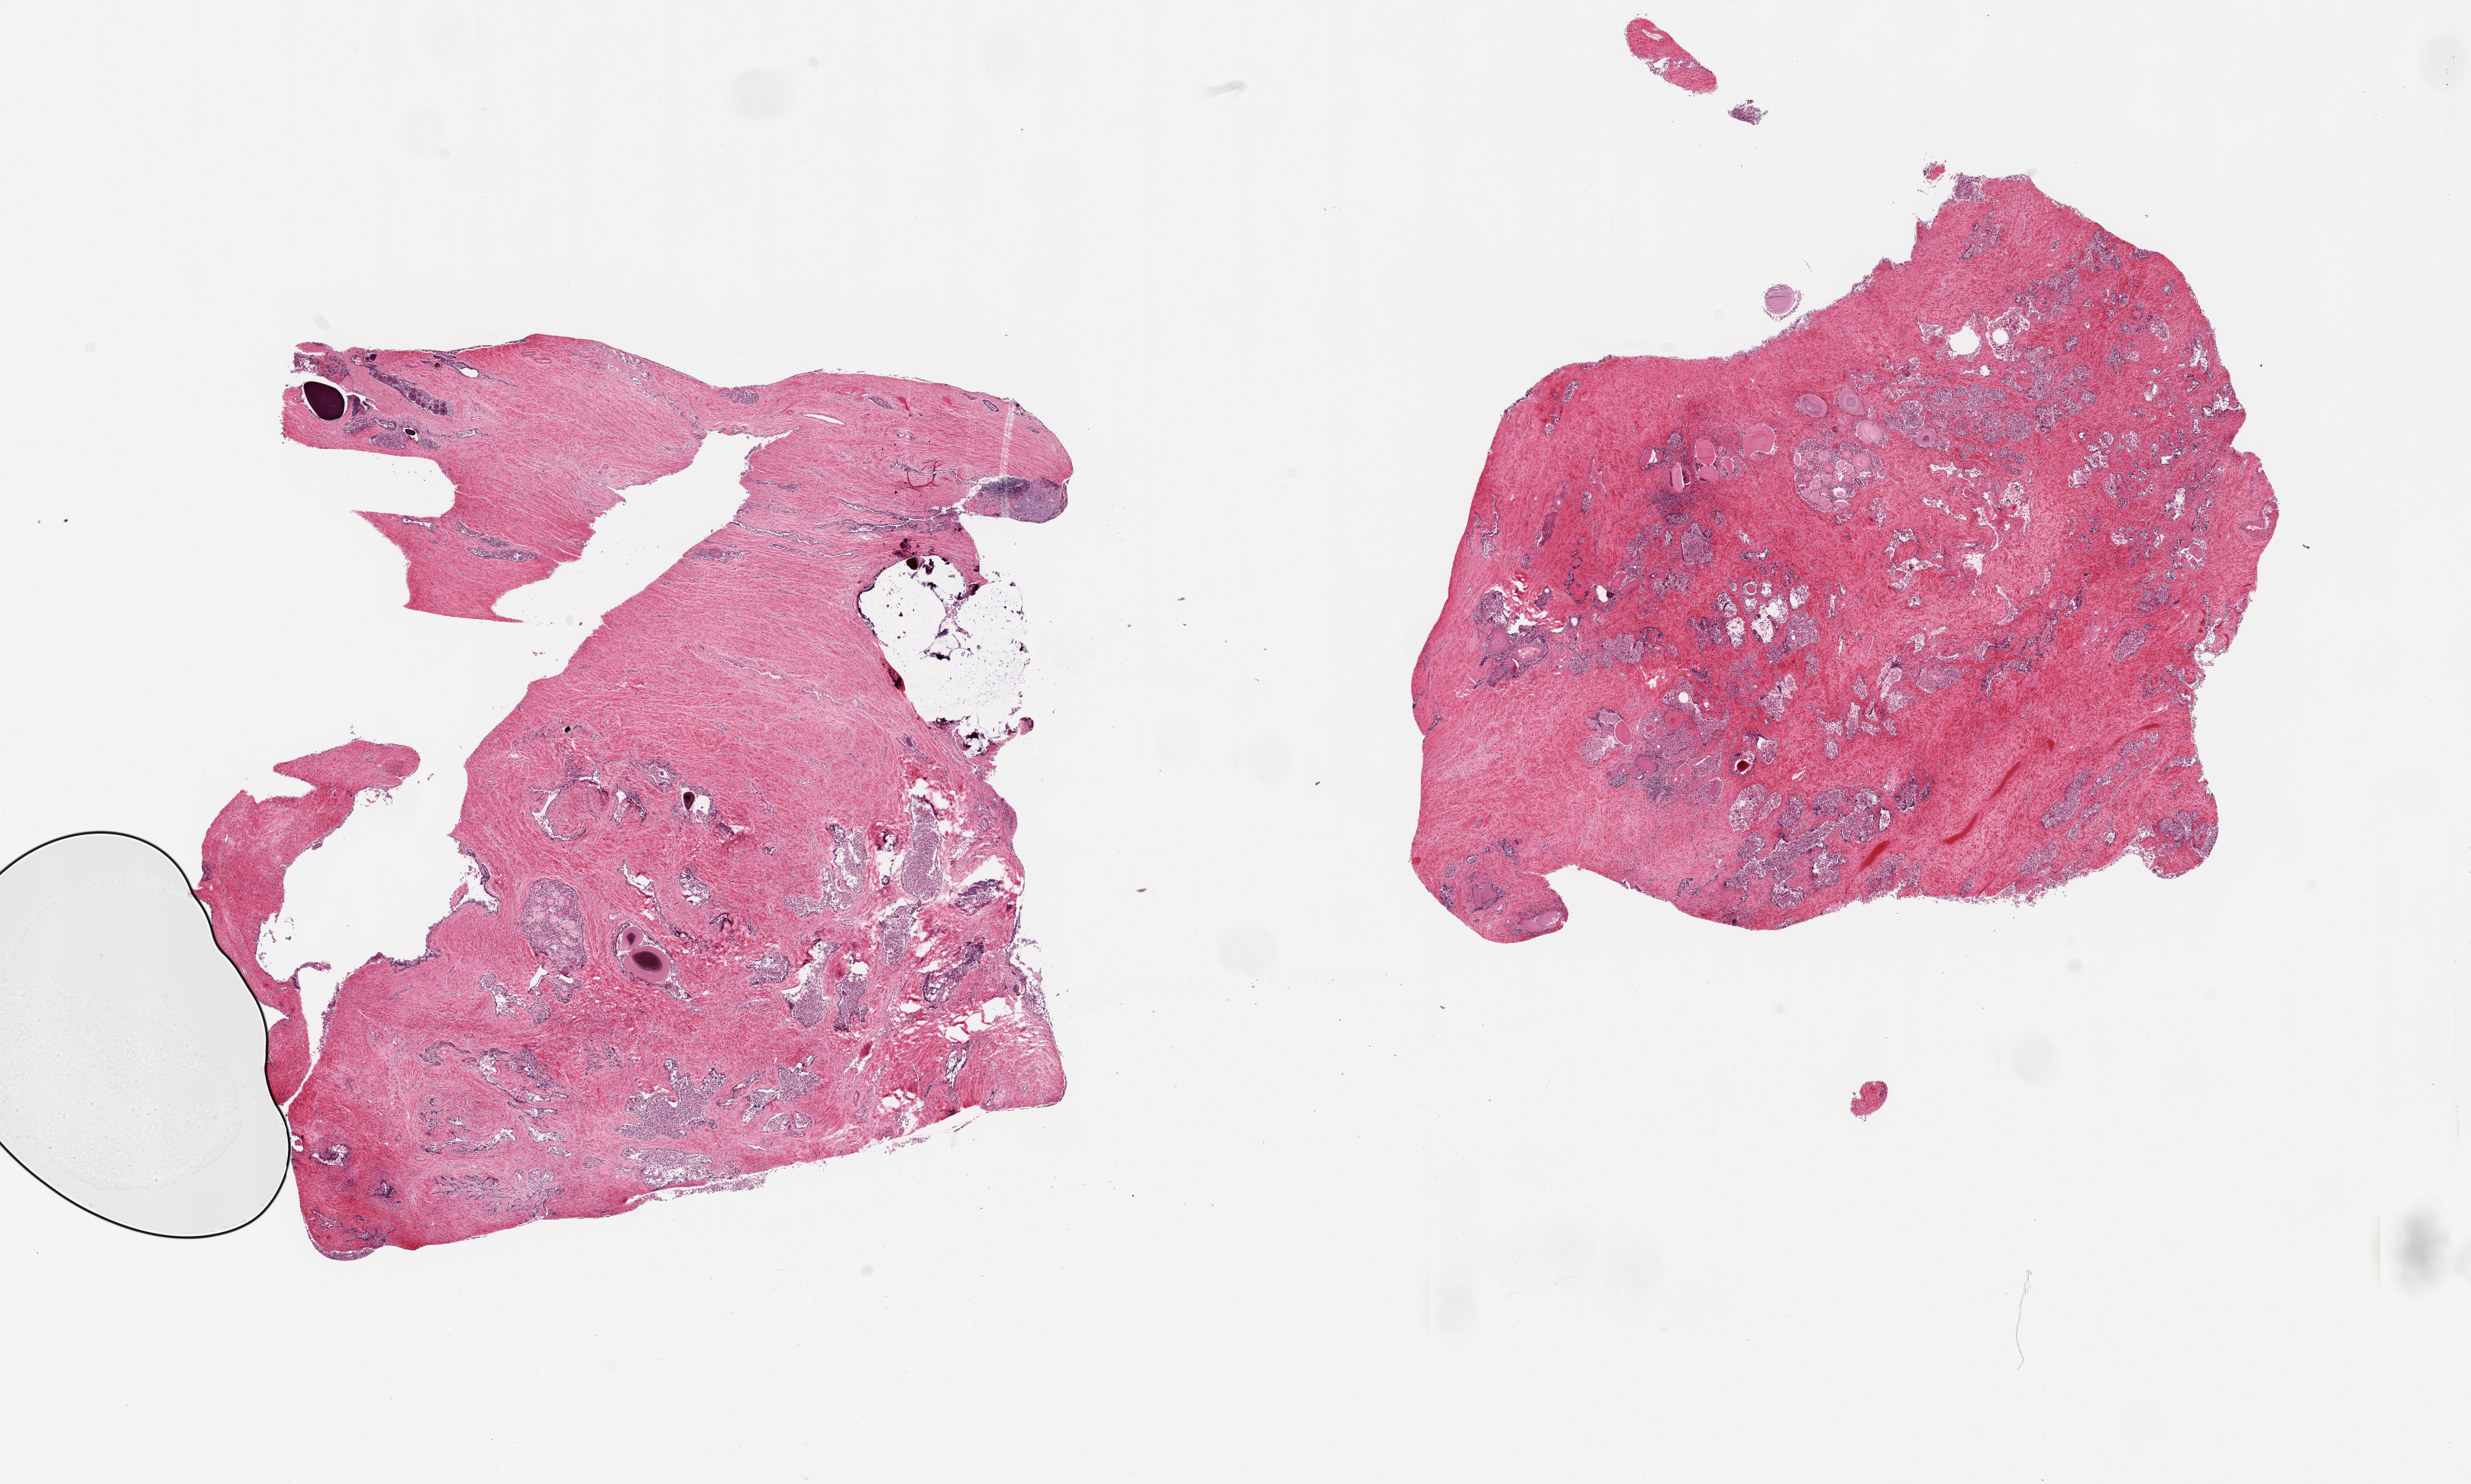
Haematoxylin and eosin whole-slide image, shown as a low-resolution overview of the whole scanned area (about 25.6 x 15.4 mm); PAXgene-fixed paraffin-embedded (PFPE) section; section of prostate (target tissue); donor tissue sample.
Pathologist's review note for this sample: 2 pieces; glands completely autolyzed.